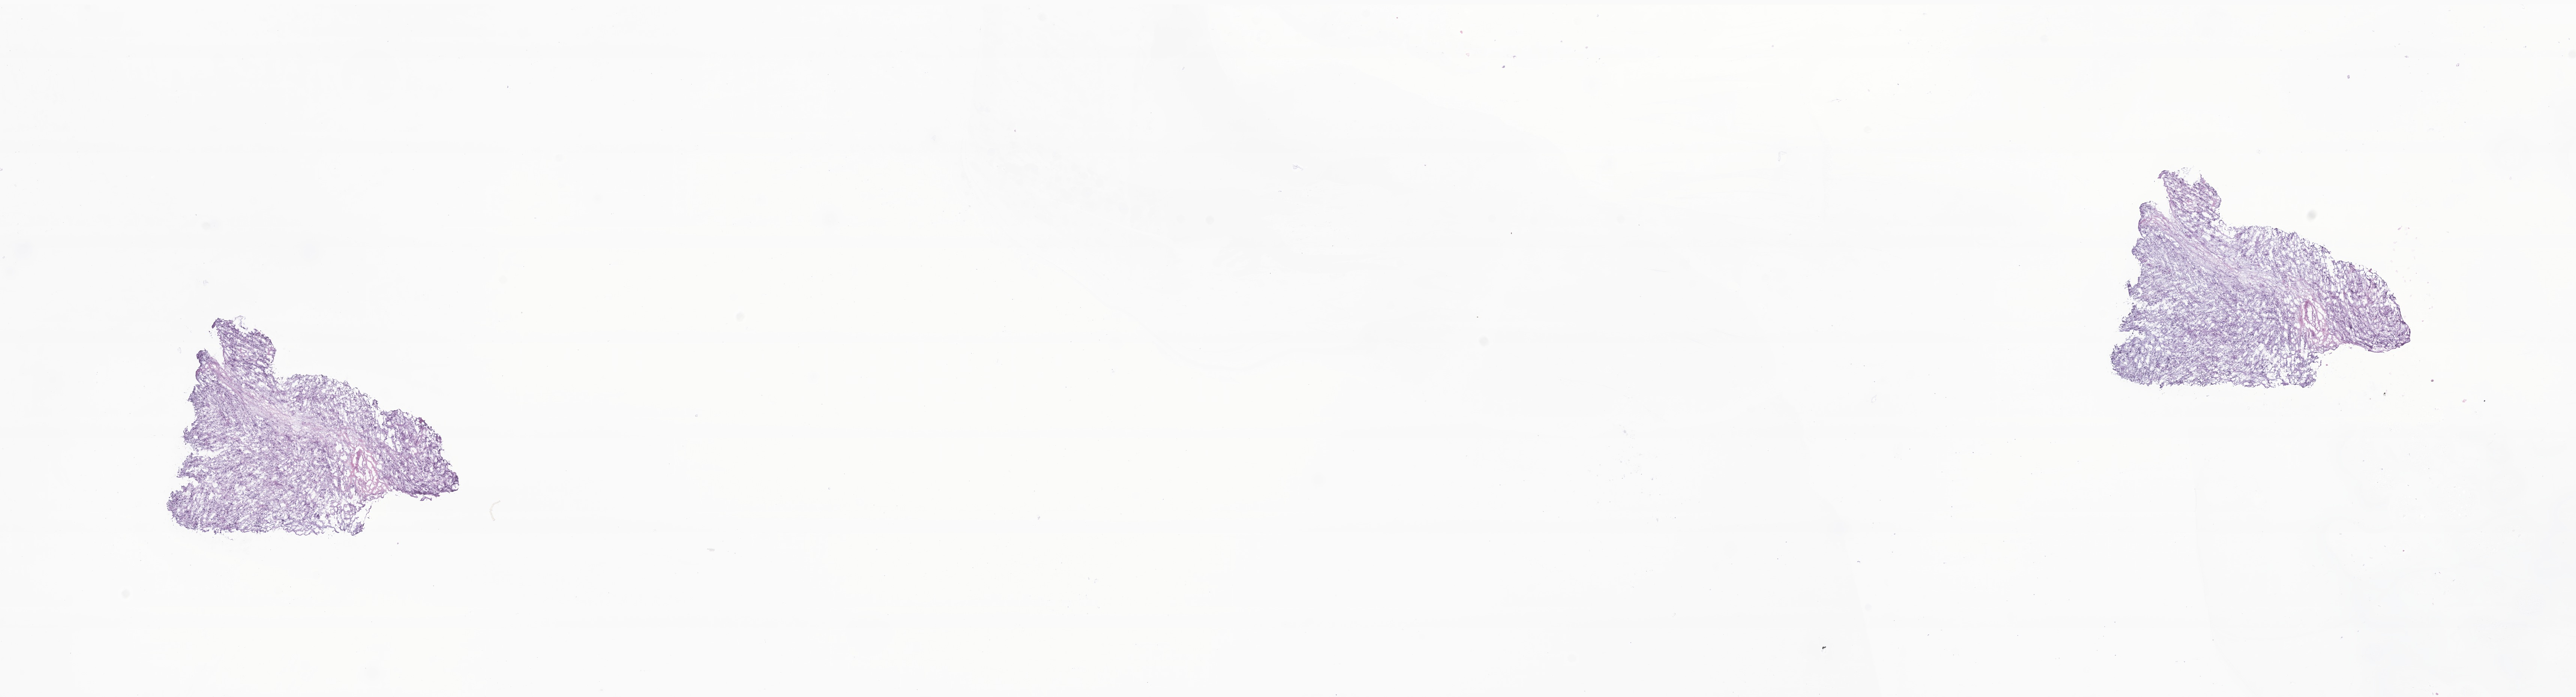
Digitized H&E-stained section of tumor tissue from the brain stem — whole scanned area (about 29.0 x 7.8 mm) shown as a low-resolution overview. Frozen section (OCT-embedded). Male patient, age 63 months (5 years 3 months).
Recorded diagnosis: Medulloblastoma, NOS.